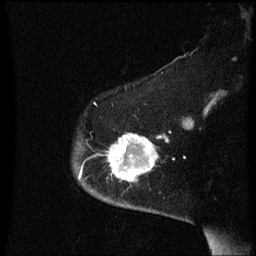
Breast MRI (dynamic contrast-enhanced), one sagittal slice. Position 48 of 60 along the scan axis. Dynamic contrast-enhanced series, image 2 of 3 at this slice position (ordered by acquisition). 1.5 T. TE 4.2 ms, TR 8.4 ms. 256 × 256 image matrix, field of view 200 × 200 mm. Patient: female, 54 years. Case-level facts recorded for this patient, not image findings: setting: breast cancer imaged before/during neoadjuvant chemotherapy; receptor status: HR-positive, HER2-negative.
Outlined on this slice (semi-automatically segmented with operator editing):
- analysis volume of interest (the breast-tissue region the enhancement analysis was run in; not a lesion): bounding box (x1, y1, x2, y2) in pixels: (108, 134, 169, 191)
- tumour enhancement mask (voxels above the 70 % enhancement threshold inside the analysis volume of interest): (108, 134, 169, 181)